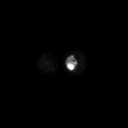
FDG PET of an extremity soft-tissue mass (from a PET/CT study), one axial slice; 128 × 128 image matrix, field of view 700 × 700 mm. Female patient, age 70 years. Case-level facts recorded for this patient, not image findings: histological type: extraskeletal high grade osteogenic sarcoma; grade: high; site of the primary tumour: left calf.
Outlined on this slice (expert contour drawn on MRI and transferred to this co-registered scan by the dataset authors):
- gross tumour volume (mass): bounding box [x1, y1, x2, y2] px = [66, 57, 77, 70]